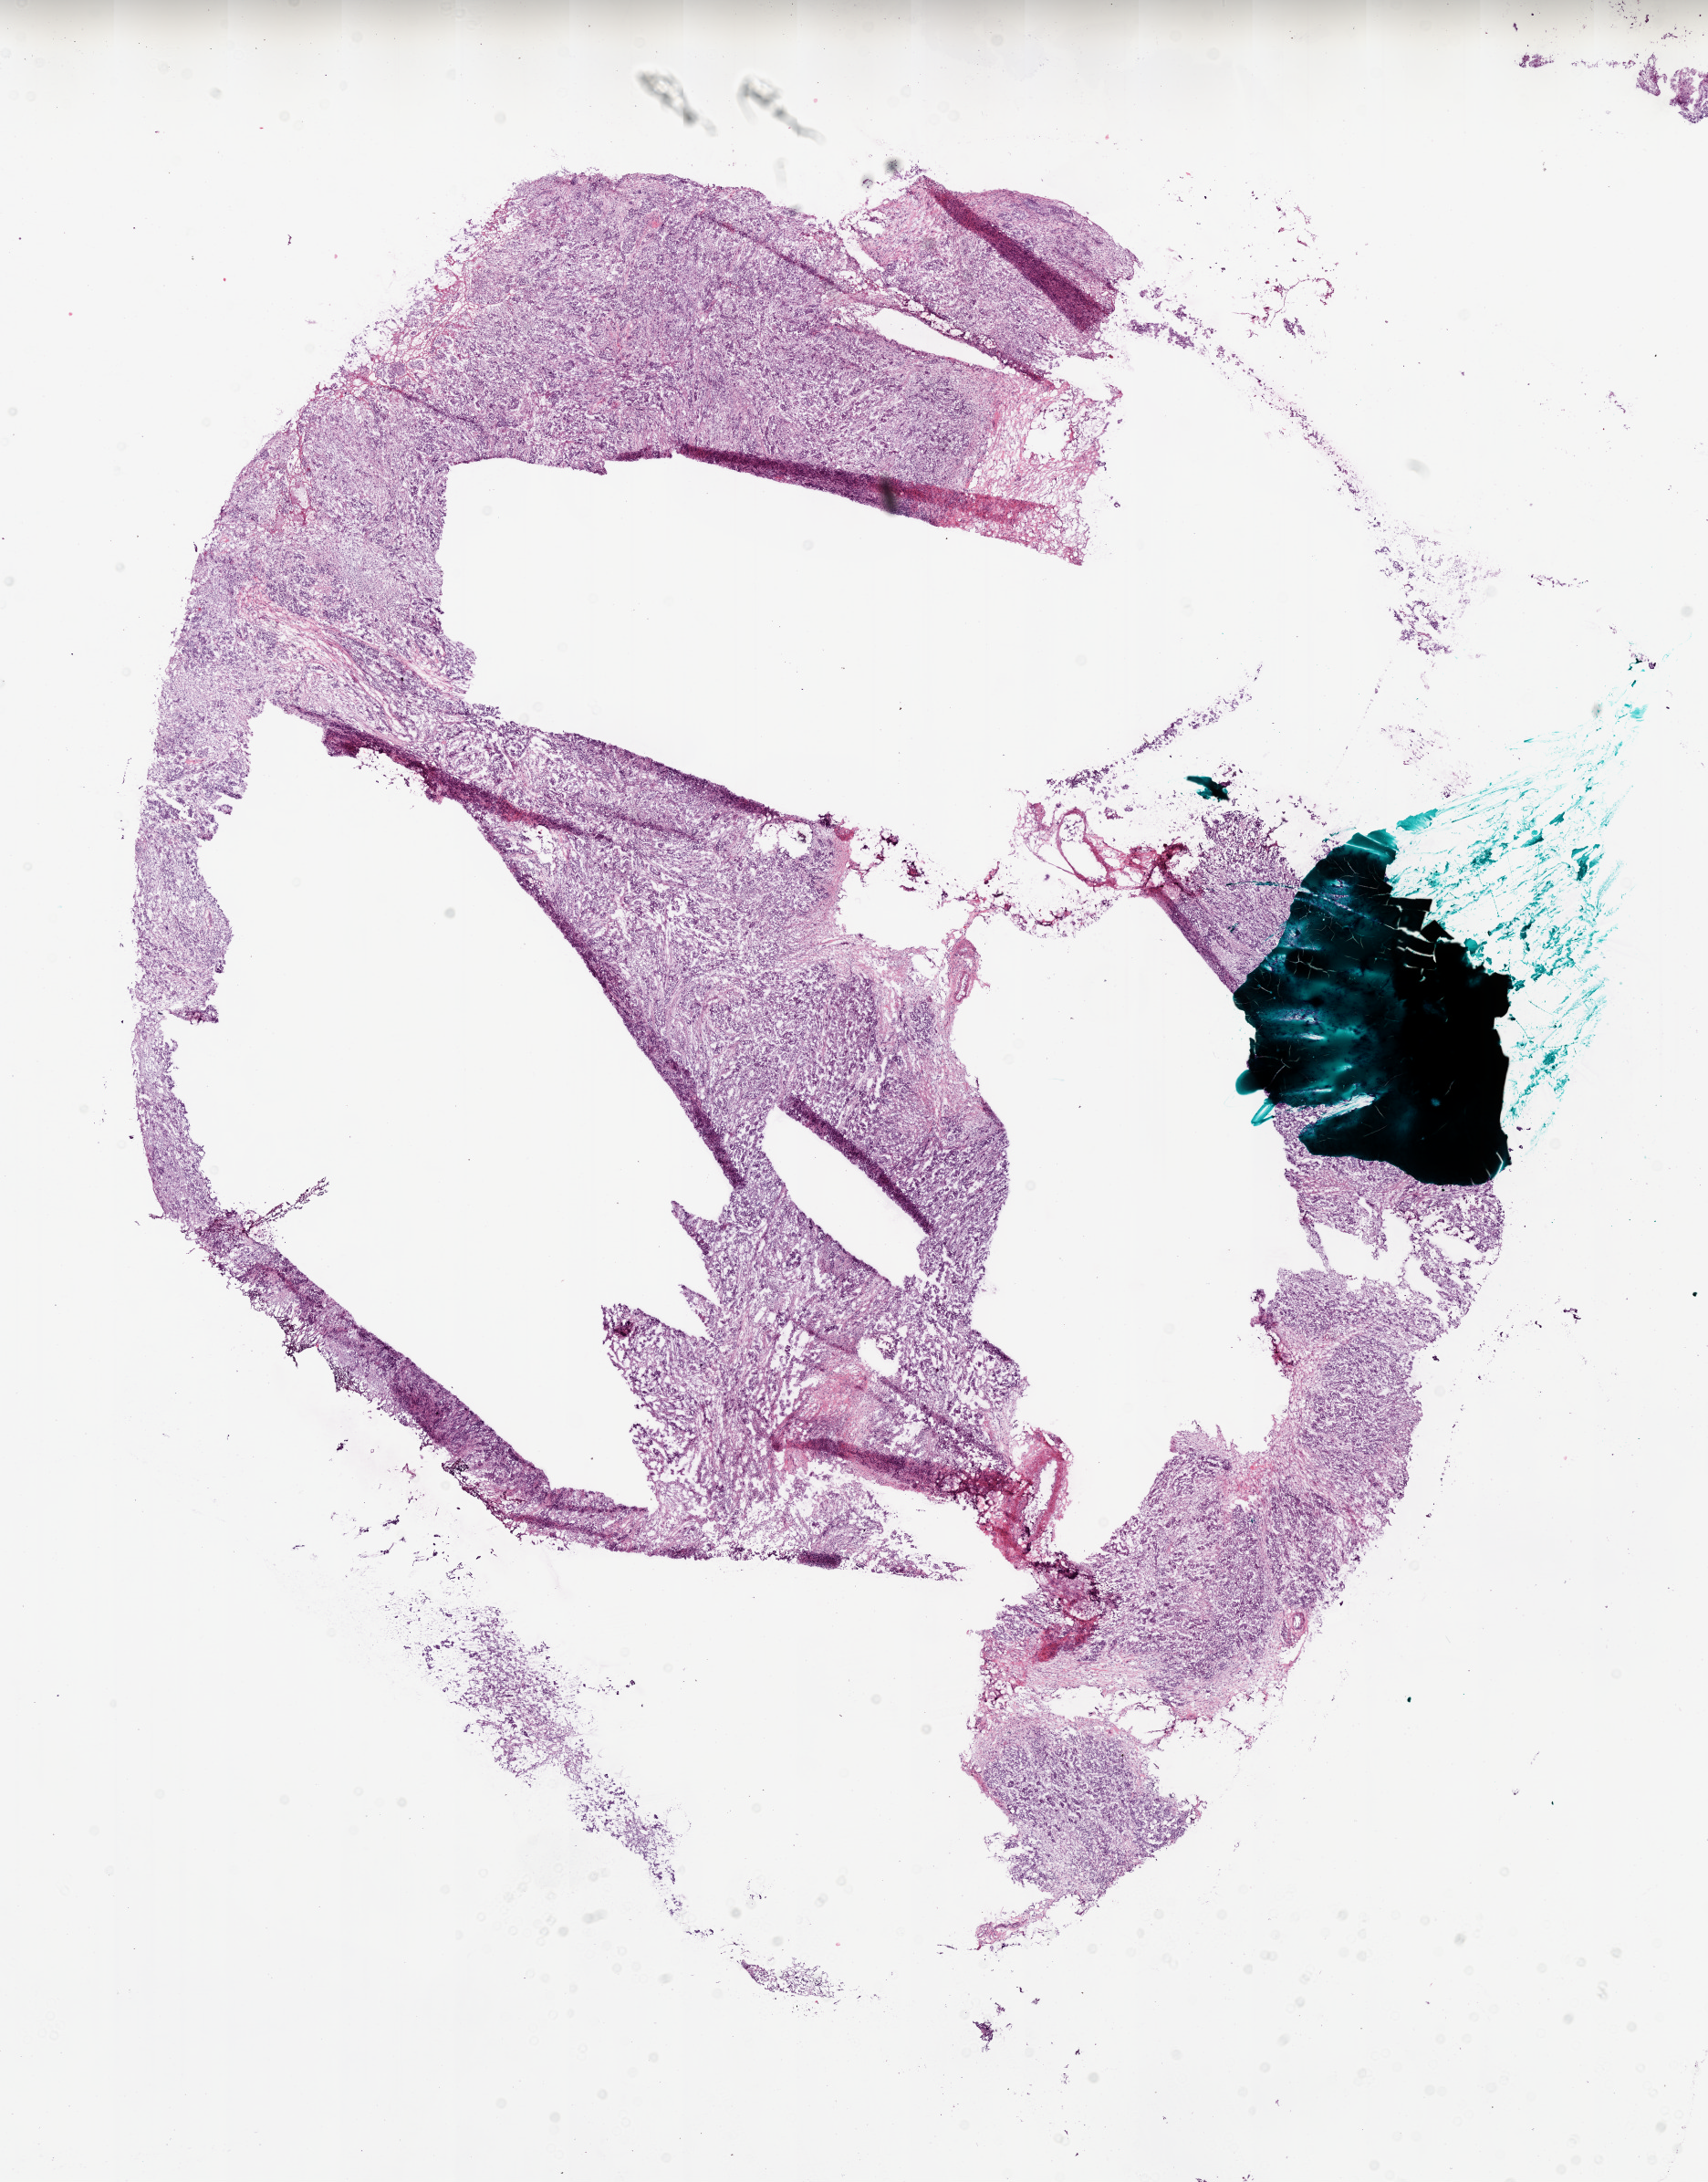
H&E whole-slide image, low-resolution overview of the scanned area, about 15.0 x 19.1 mm (acquisition: 20x scan), frozen section from the bottom of the tissue portion, sample: primary tumour, ovary. Female, age 56 years at initial diagnosis. Histologic grade: G3 (poorly differentiated). Slide review estimates, as recorded: tumour cells 79%, tumour nuclei 80%, normal cells 20%, stromal cells 0%, necrosis 1%.
FIGO stage: IIIC. Pathologic diagnosis: Serous cystadenocarcinoma, NOS. Laterality: bilateral.